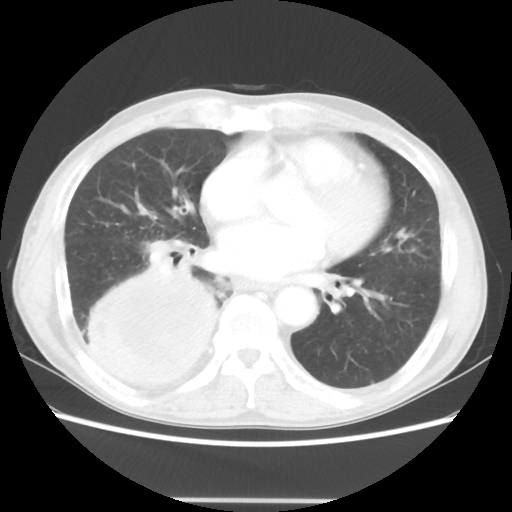
Chest CT, one axial slice. Slice 18 of 48 in the series (ordered by position). 100 kVp. Lung window (W 1500 / L -600 HU). 5 mm slice thickness. 512 × 512 image matrix, field of view 361 × 361 mm. Male patient, age 66 years. Case-level facts recorded for this patient, not image findings: clinical TNM (as recorded): T4 N1 M1; histopathological grade: G3.
Outlined on this slice (rectangle marked by the reading radiologist):
- lung tumour (recorded histology: small cell carcinoma): box from (x=81, y=265) to (x=222, y=390) px